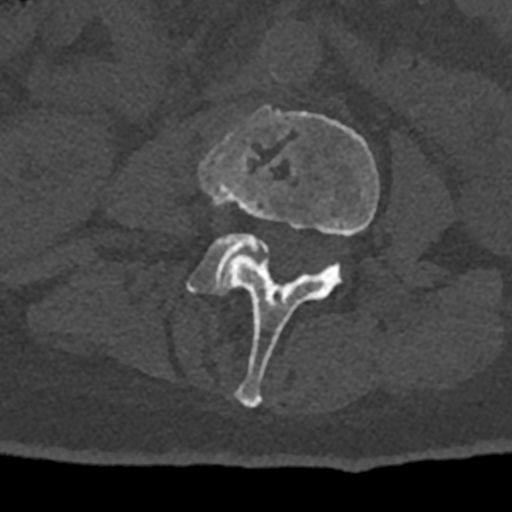
CT including the spine, one axial slice. Slice 305 of 797 in the series (ordered by position). 120 kVp. Bone window (W 1800 / L 400 HU). 0.5 mm slice thickness. 512 × 512 image matrix, field of view 160 × 160 mm. Male patient, age 74 years. Case-level facts recorded for this patient, not image findings: primary cancer: renal.
Outlined on this slice (semi-automatic segmentation, software-assisted and operator-edited):
- L3 vertebra: bounding box <199,108,379,408> (left, top, right, bottom; pixels)
- L4 vertebra: <187,233,269,295>